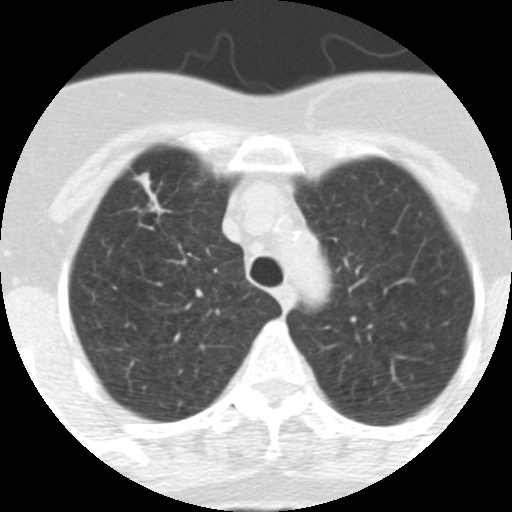
Axial slice from a low-dose chest CT screening exam; first (baseline) screen; lung window (W 1500 / L -600 HU); 2.5 mm slice thickness; slice 65 of 313 in the series. Female participant, aged 62 years at enrolment.
Expert-annotated lung lesion, bounding box (x1, y1, x2, y2) in pixels: (116, 167, 187, 236). Screening reader's record for this exam (one nodule recorded; not confirmed to be the boxed lesion): non-calcified nodule or mass ≥4 mm, right upper lobe, 9 × 7 mm, spiculated (stellate) margins, soft tissue attenuation. Official screen result: positive, change unspecified: nodule(s) >= 4 mm or enlarging nodule(s), mass(es), or other non-specific abnormalities suspicious for lung cancer. Lung cancer was diagnosed 126 days after this screen: adenocarcinoma, NOS, right upper lobe, moderately differentiated (G2), stage IA (AJCC 6th edition), 18 mm at pathology.